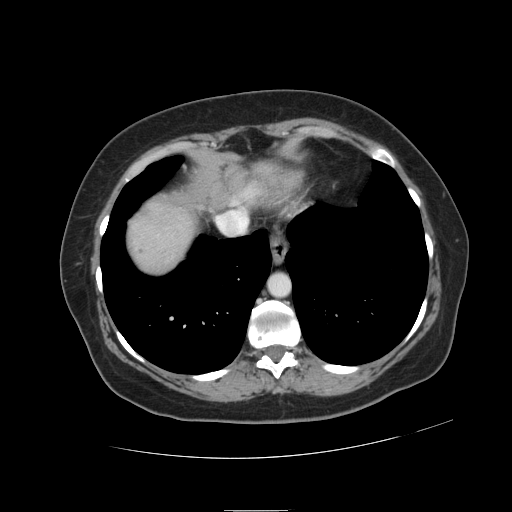
Contrast-enhanced abdominal CT, one axial slice. Slice 109 of 121 in the series (ordered by position). 120 kVp. Intravenous contrast given. Soft-tissue window (W 400 / L 40 HU). 512 × 512 image matrix. Female patient, age 52 years. Case-level facts recorded for this patient, not image findings: diagnosis: colorectal cancer liver metastases, imaged before liver resection; multiple liver metastases: yes; largest metastasis: 6.3 cm; disease in both lobes: no.
Outlined on this slice (manually delineated by an expert):
- liver: bounding box <128,201,196,274> (left, top, right, bottom; pixels)